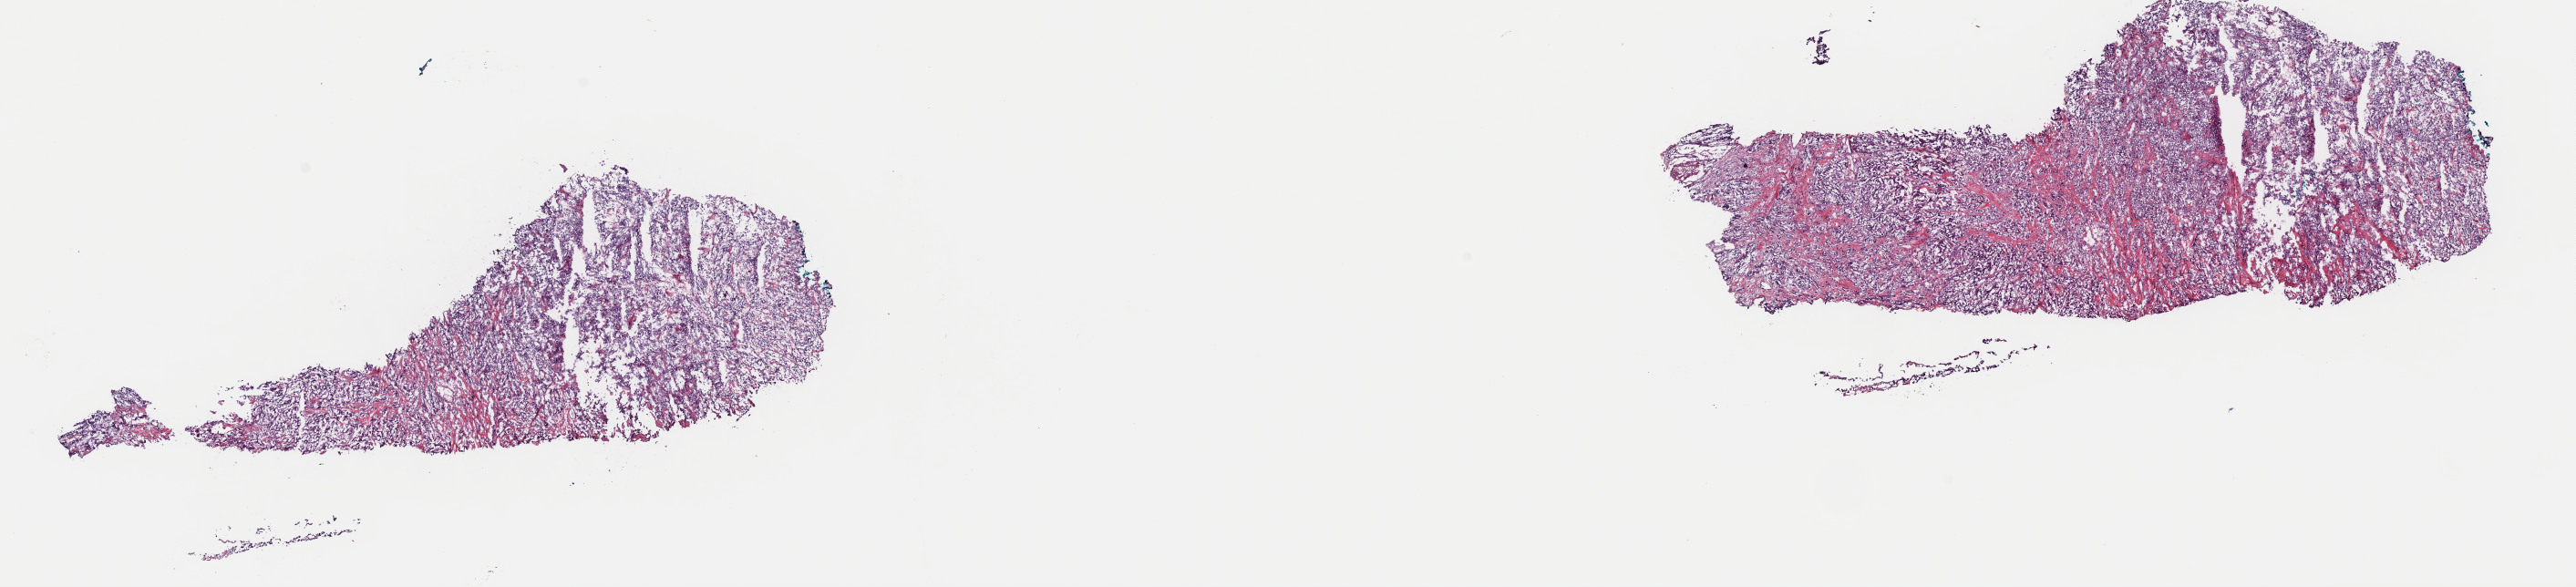
Digitized Hematoxylin and eosin (H&E) stained tissue section (whole slide) — whole scanned area (about 22.3 x 5.1 mm, from a 40x scan) shown as a low-resolution overview. Frozen section from the top of the tissue portion. Sample: primary tumour, adrenal gland. Male, age 53 years at initial diagnosis. Slide review estimates, as recorded: tumour cells 100%, tumour nuclei 75%, normal cells 0%, stromal cells 0%, necrosis 0%. Inflammatory infiltration, as recorded: lymphocyte infiltration 1%, monocyte infiltration 0%, neutrophil infiltration 0%.
Laterality: right. Diagnosis: Pheochromocytoma, NOS.